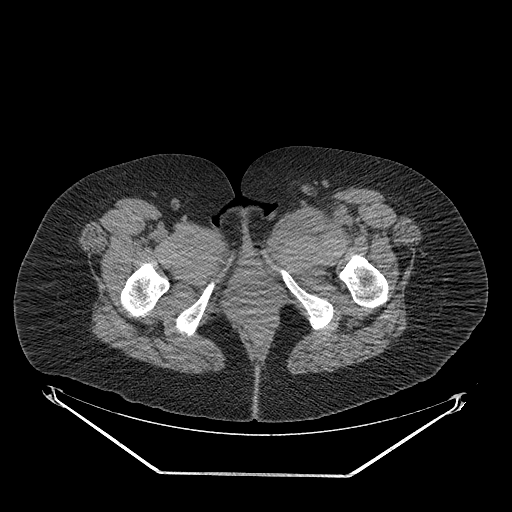
CT of an extremity soft-tissue mass (from a PET/CT study), one axial slice. Position 45 of 267 along the scan axis. 140 kVp. Soft-tissue window (W 400 / L 40 HU). 3.75 mm slice thickness. 512 × 512 image matrix. Female patient. Case-level facts recorded for this patient, not image findings: histological type: myxofibrosarcoma; grade: intermediate; site of the primary tumour: left thigh.
Annotated regions visible in this slice (expert contour drawn on MRI and transferred to this co-registered scan by the dataset authors):
- gross tumour volume including surrounding oedema: bounding box <265,205,366,252> (left, top, right, bottom; pixels)
- gross tumour volume (mass): <295,206,328,234>